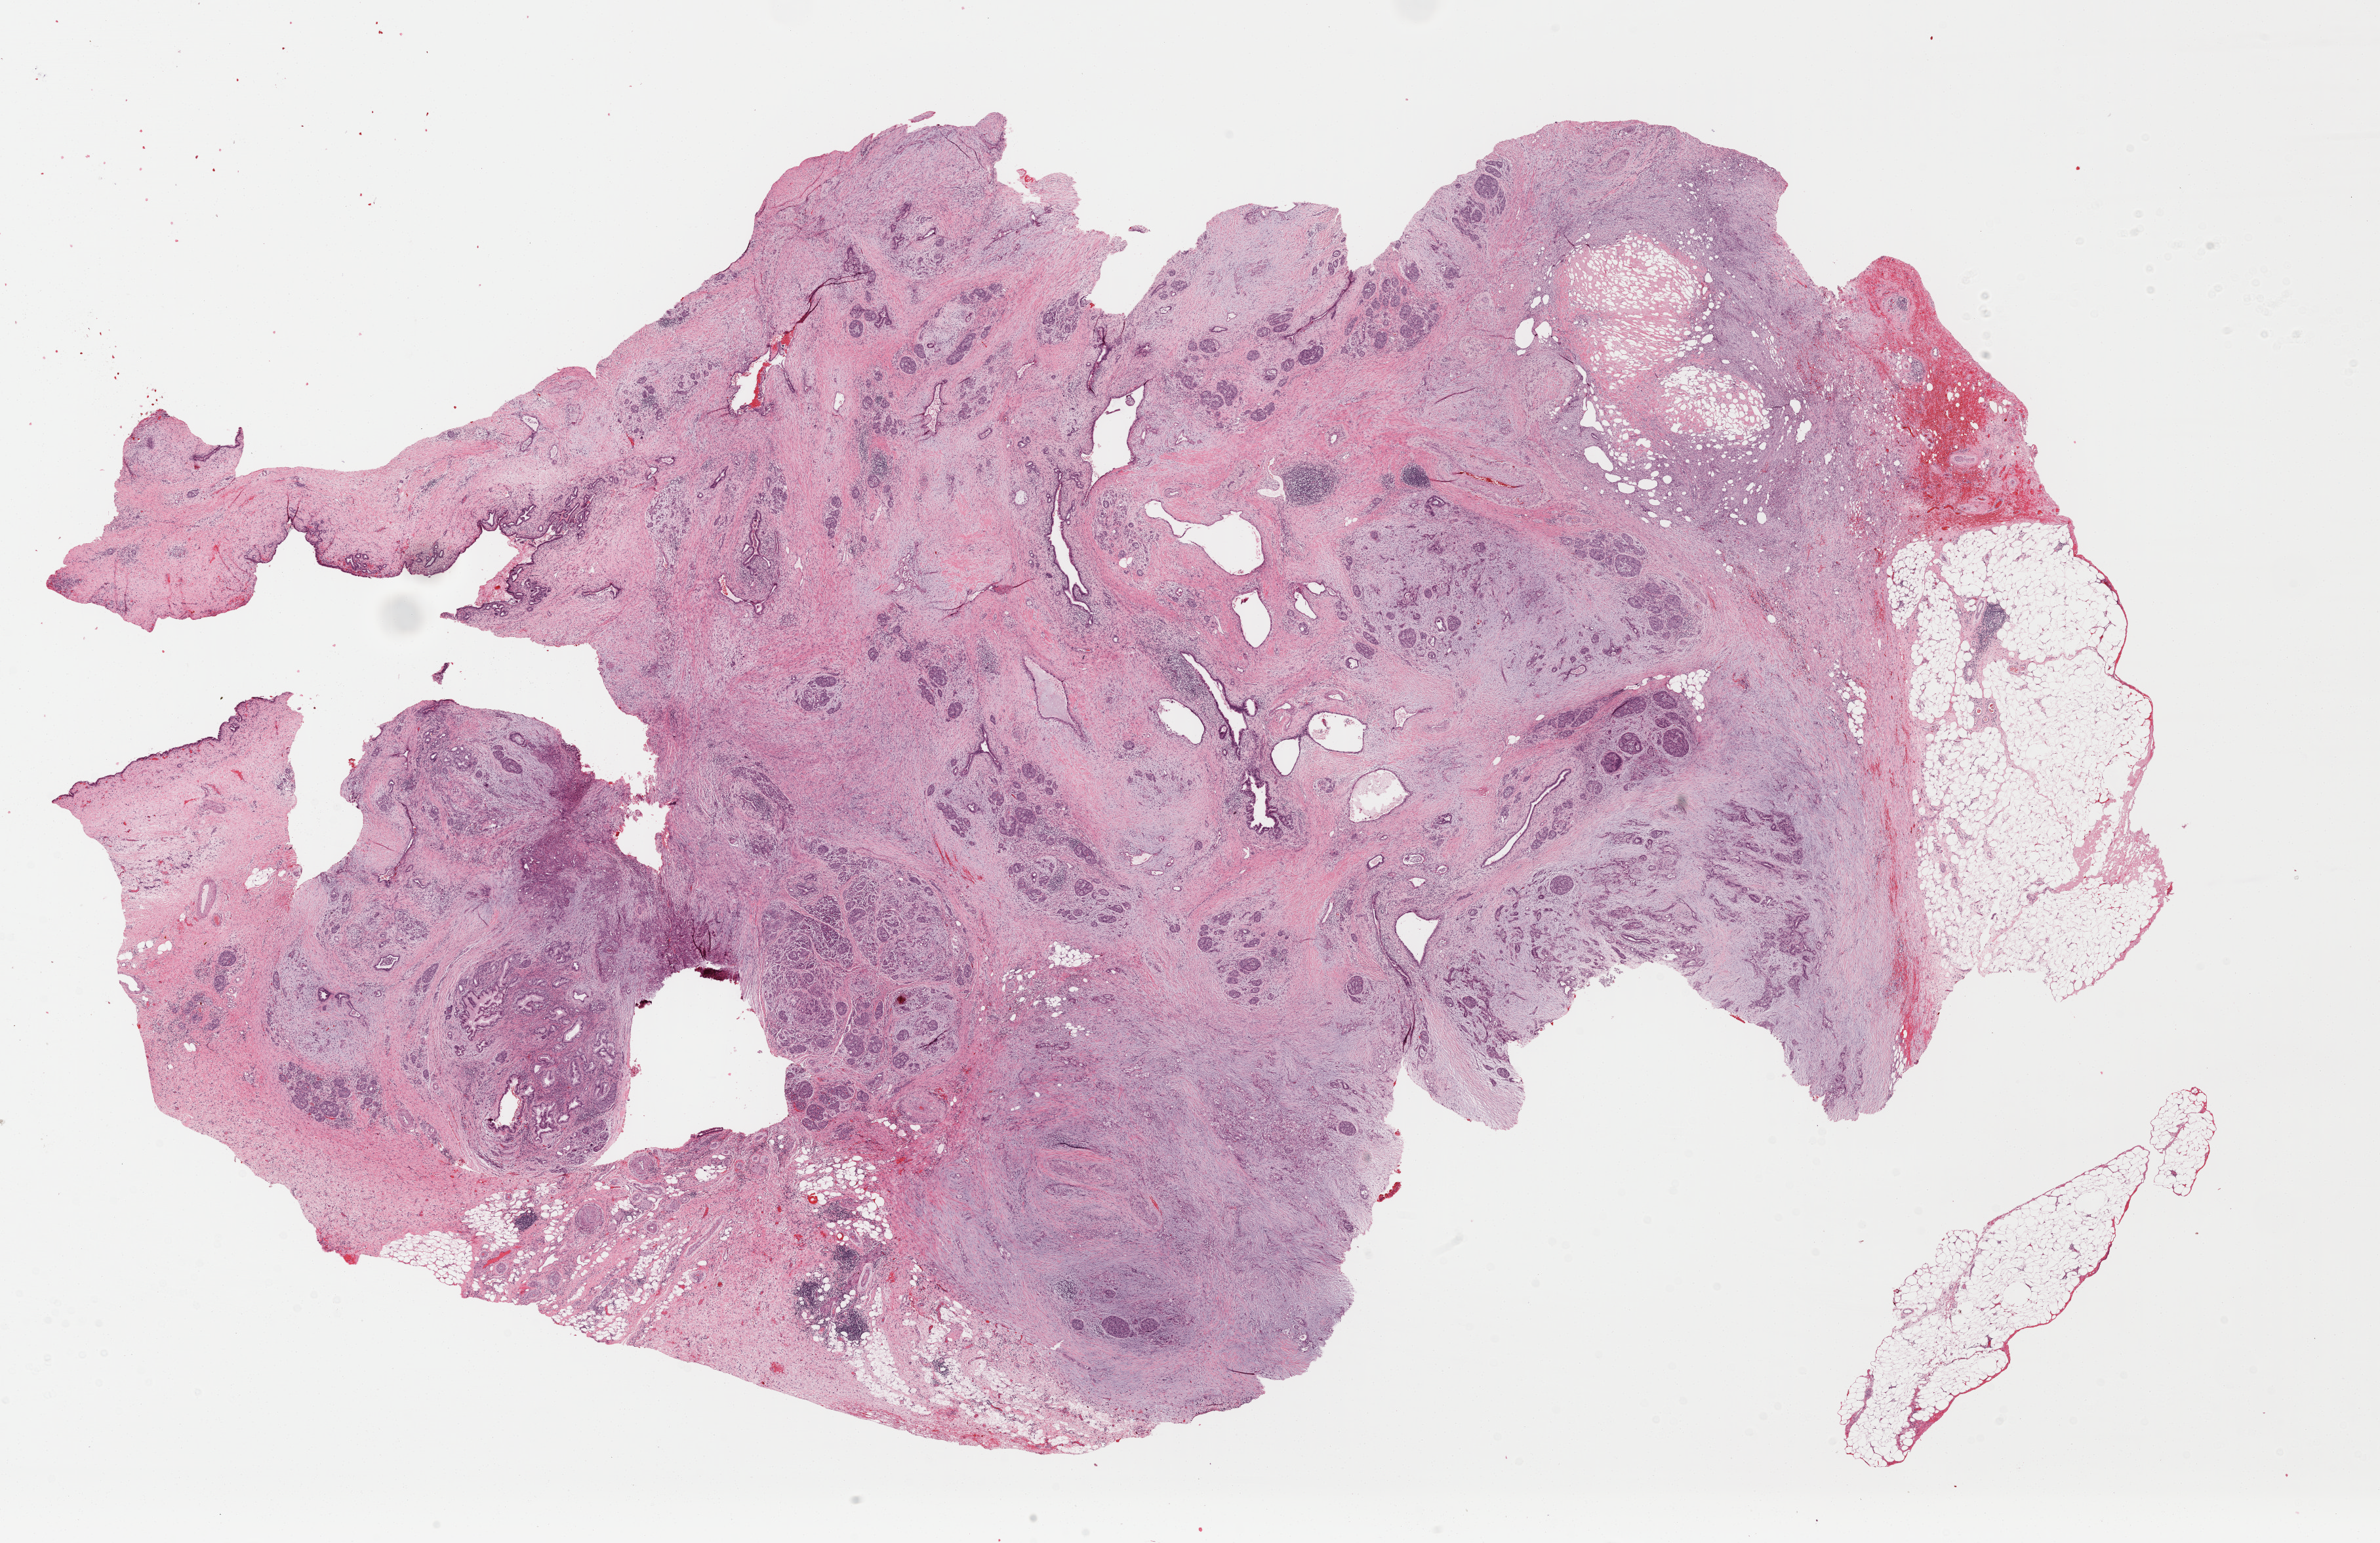
Whole-slide histology image, H&E, whole scanned area (about 28.6 x 18.6 mm) shown as a low-resolution overview, formalin-fixed paraffin-embedded (FFPE) diagnostic section, sample: primary tumour, pancreas. Male patient; age at initial diagnosis 58 years. Histologic grade: G2 (moderately differentiated).
Lymph nodes positive (case pathology): 4 of 18 examined. AJCC pathologic stage: IIB (7th edition). Pathologic diagnosis: Infiltrating duct carcinoma, NOS (head of pancreas).